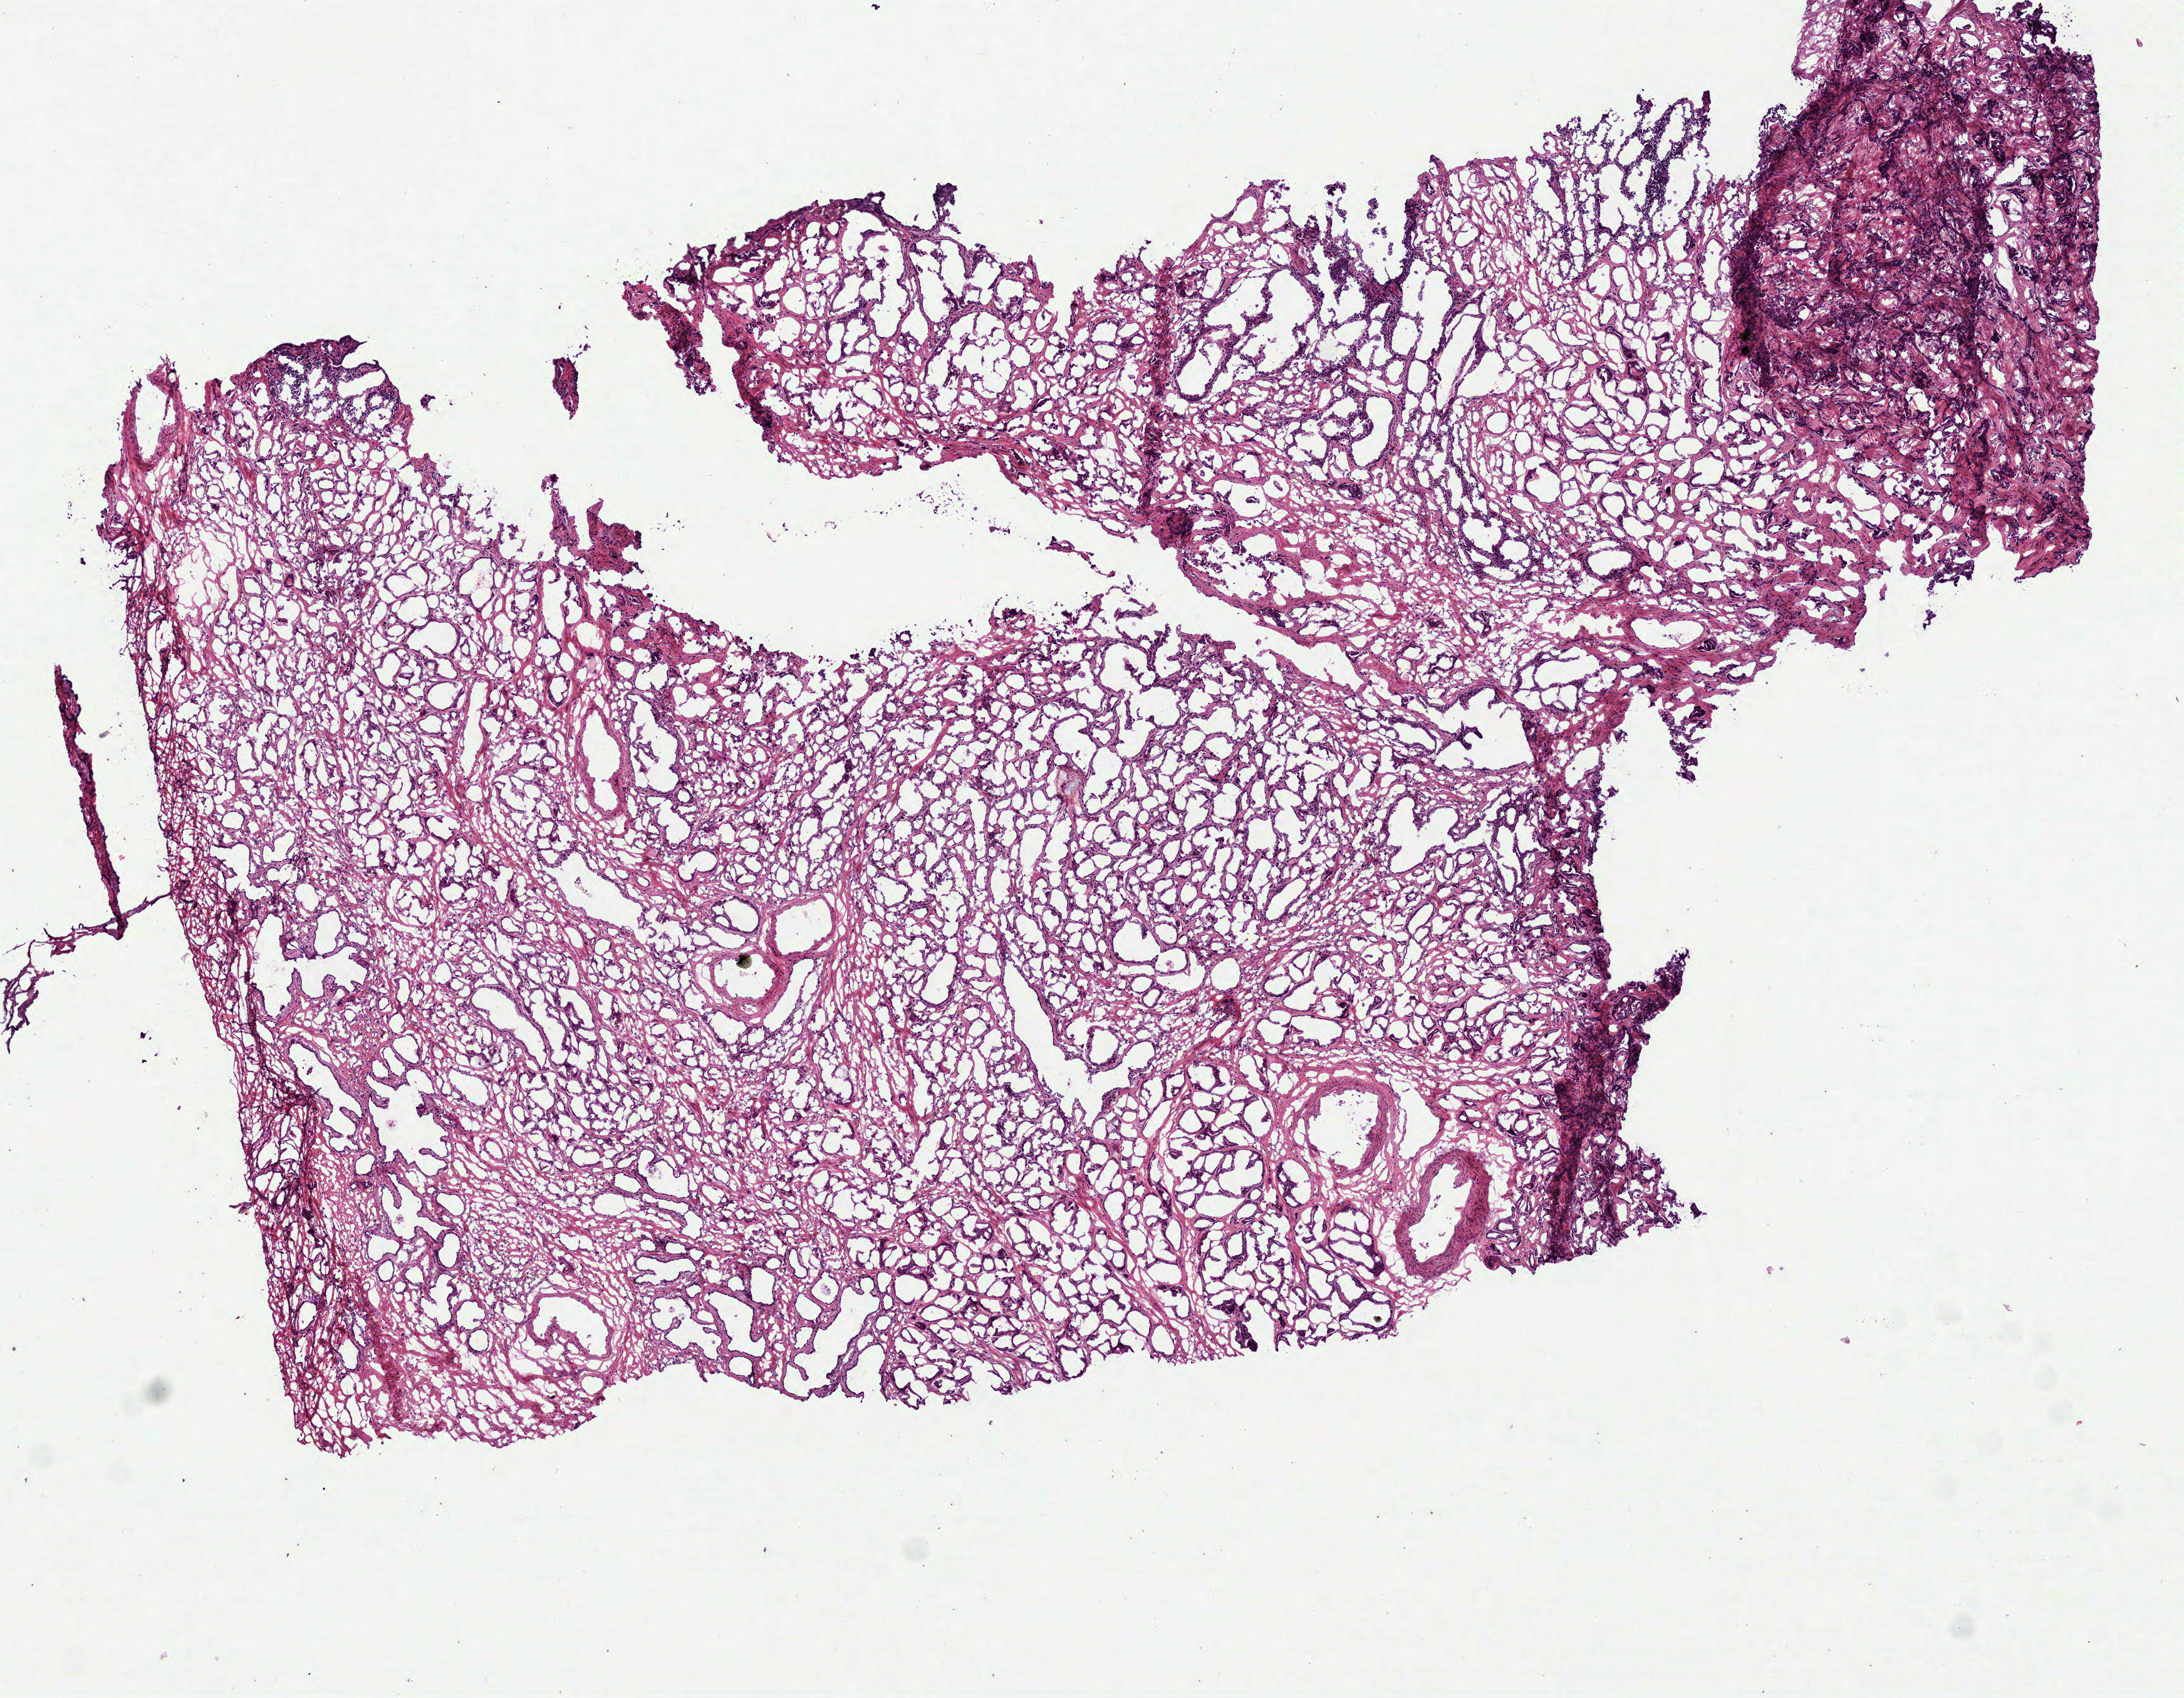
Whole-slide histology image, H&E — shown as a low-resolution overview of the whole scanned area (about 7.0 x 5.5 mm, slide scanned at 40x), frozen section from the bottom of the tissue portion, primary tumour sample from the prostate. Patient: male, age at initial diagnosis 68 years. Gleason score: 7 (4+3). Pathologist review of this section (percent, as recorded): tumour cells 60%, tumour nuclei 60%, normal cells 20%, stromal cells 20%, necrosis 0%. Inflammatory infiltration, as recorded: lymphocyte infiltration 4%, monocyte infiltration 0%, neutrophil infiltration 0%.
* laterality: bilateral
* pathologic diagnosis: Acinar cell carcinoma (prostate gland)